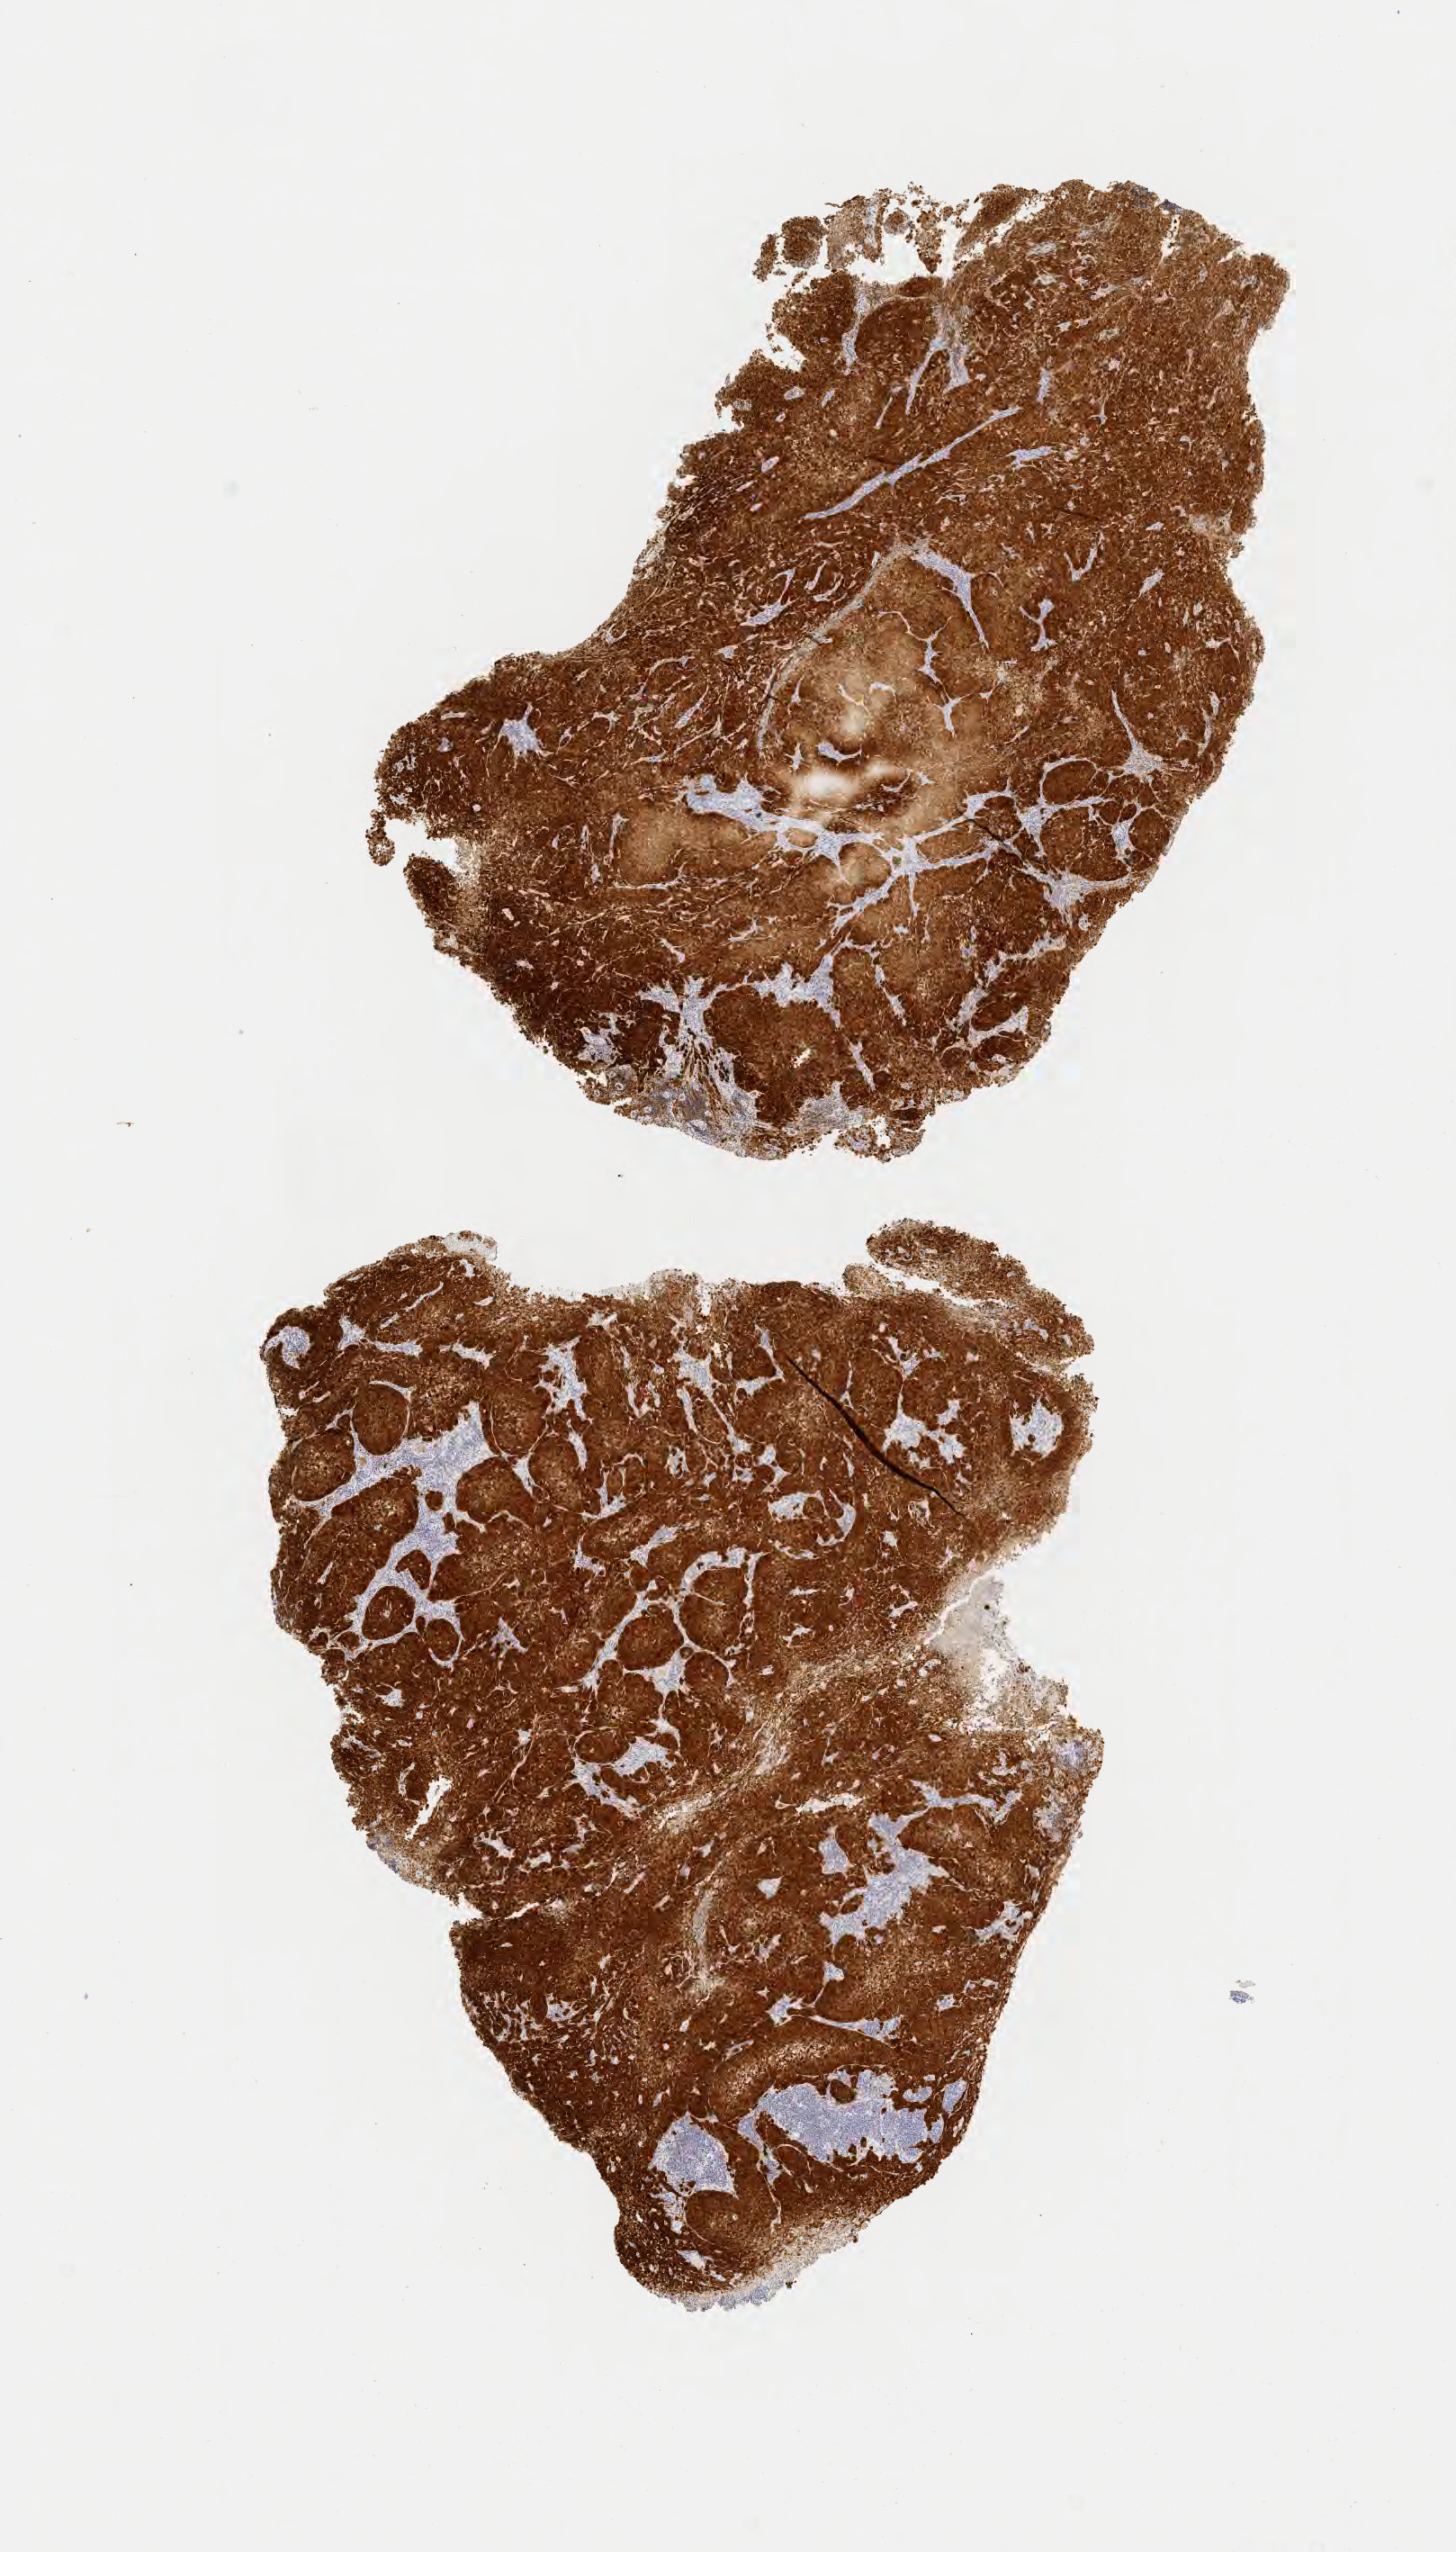
Whole-slide image, immunohistochemical stain for p16 (p16INK4a) — low-resolution overview of the scanned area, about 6.5 x 11.5 mm. Tumor tissue. Site: cervix. Female patient, age 45 years.
Histologic diagnosis: Squamous cell carcinoma, large cell, nonkeratinizing, NOS.